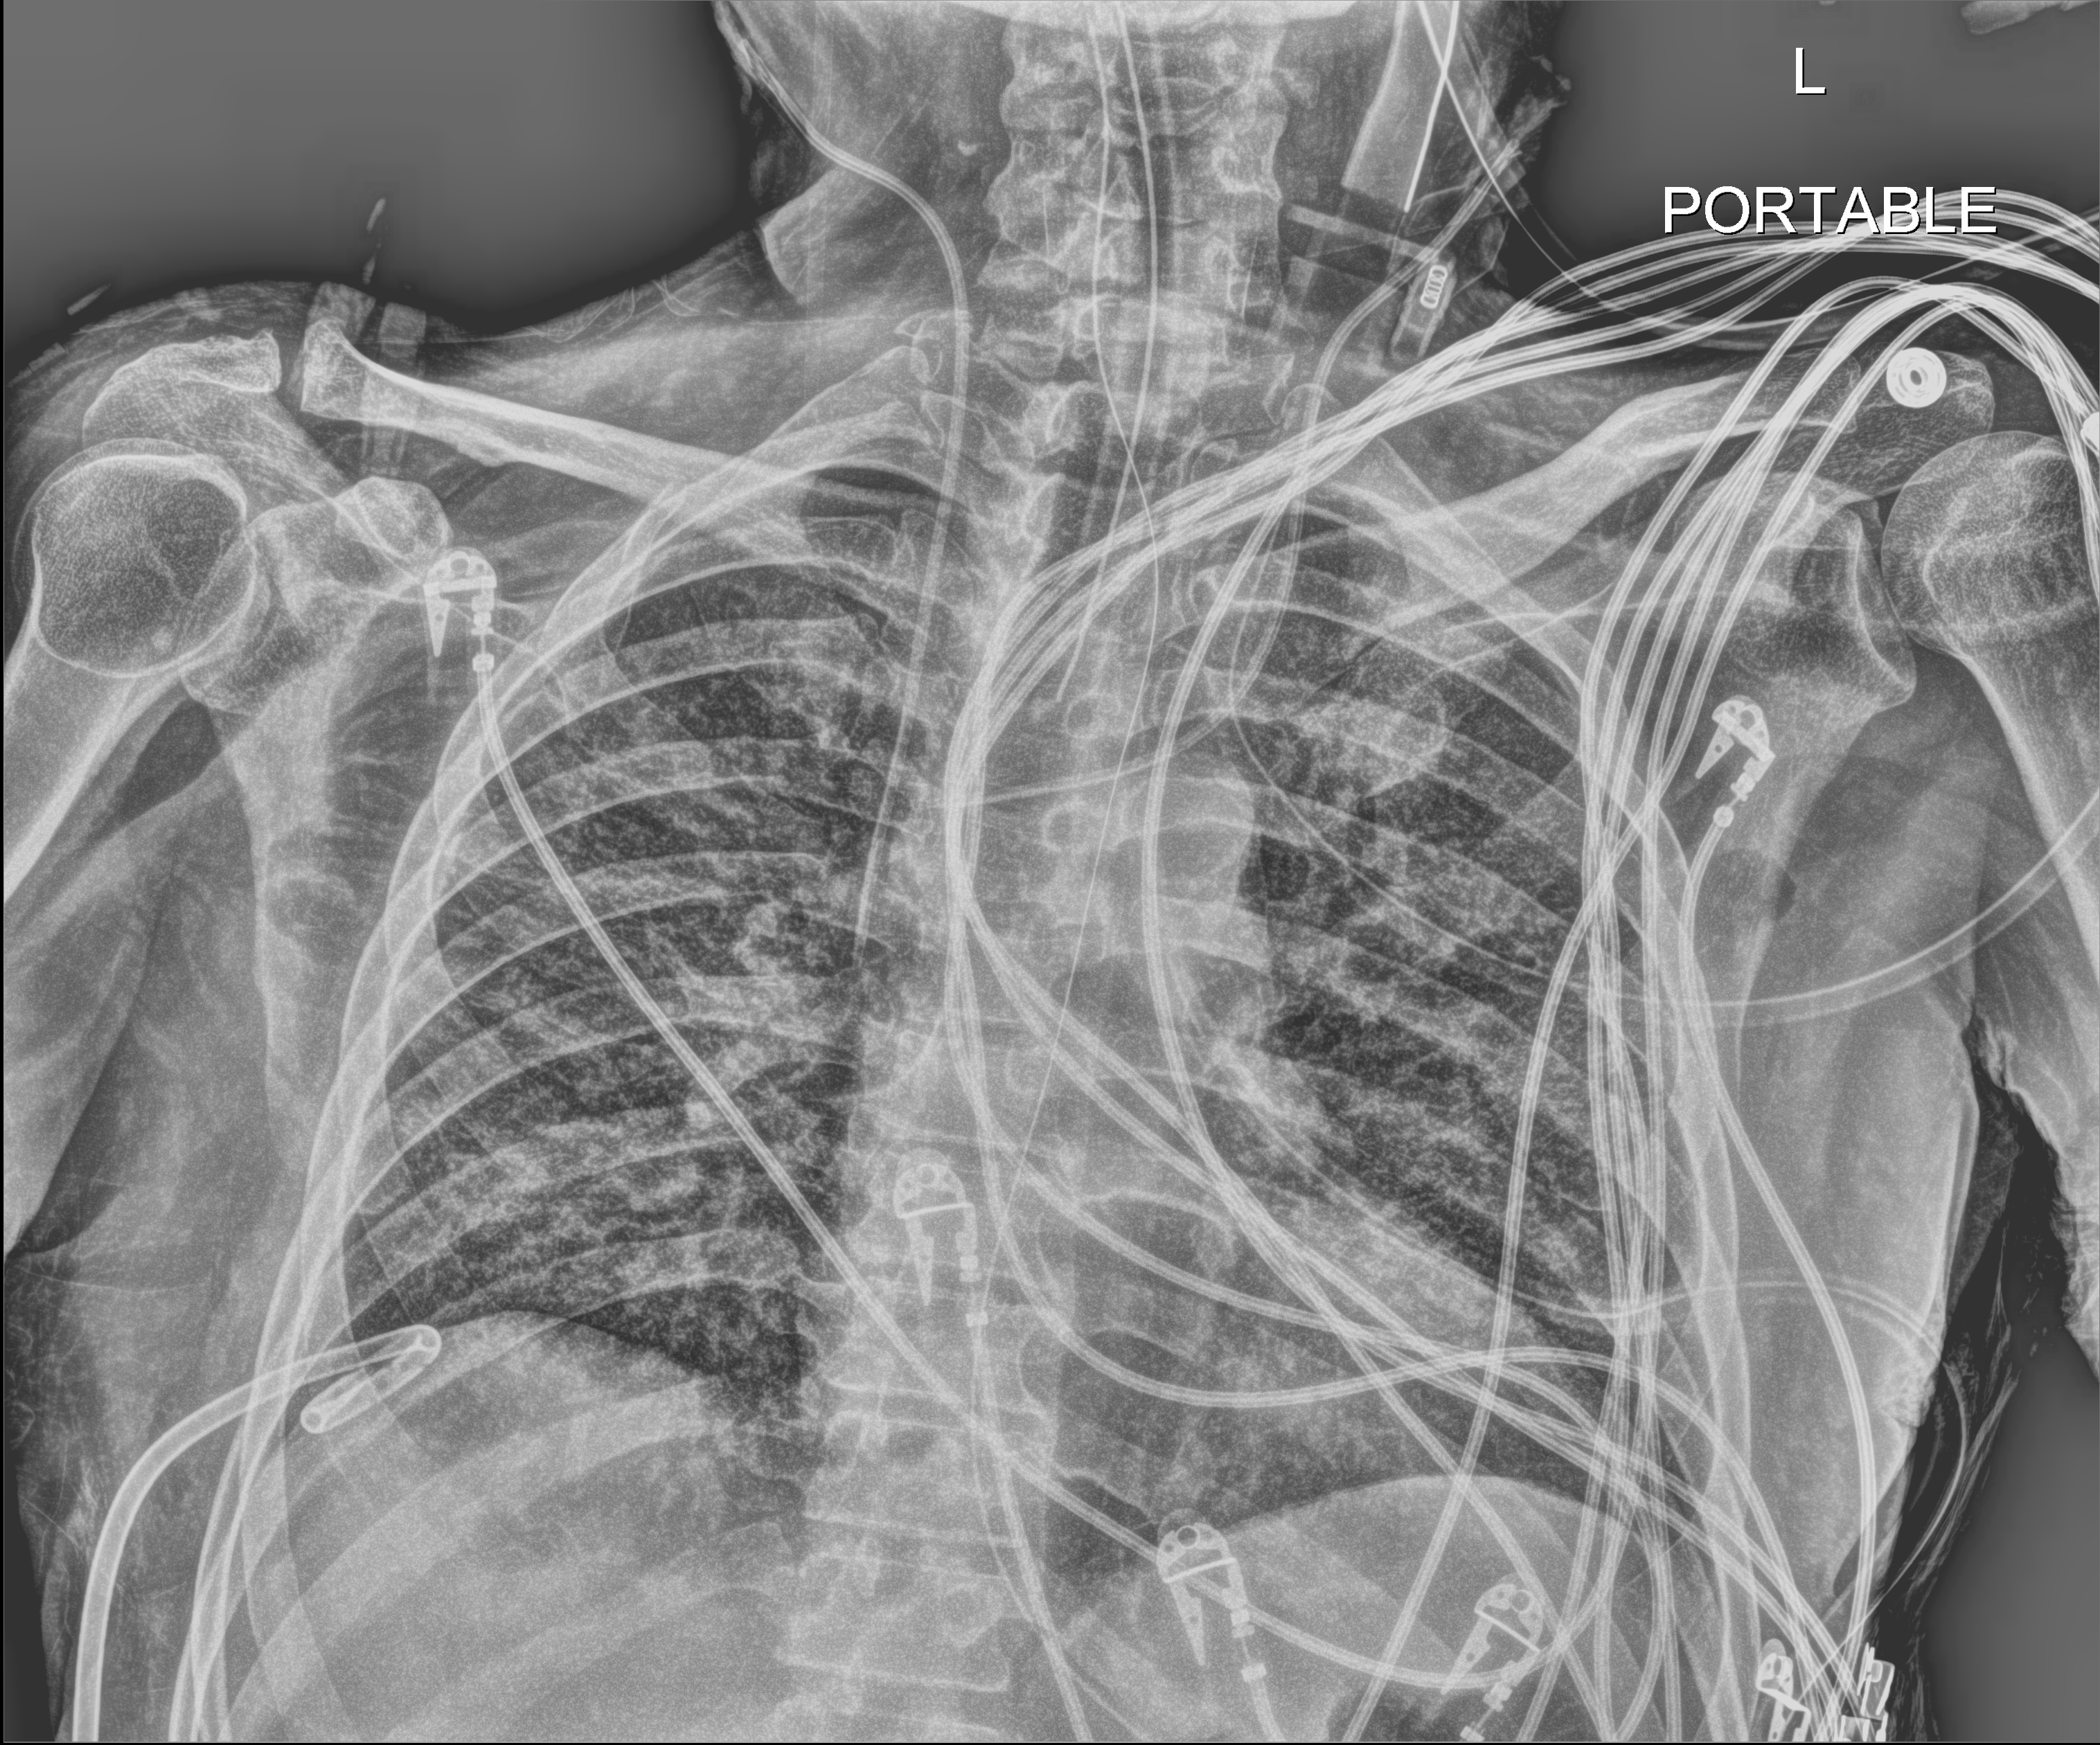
Chest X-ray (portable), anteroposterior (AP) projection. Patient hospitalised with COVID-19; male, aged 18–59 years.
From the hospital-stay record, not from the radiograph (when in the stay this image was taken is not recorded):
- other chronic lung disease (admission record): no
- admitted to intensive care during this hospital stay: yes